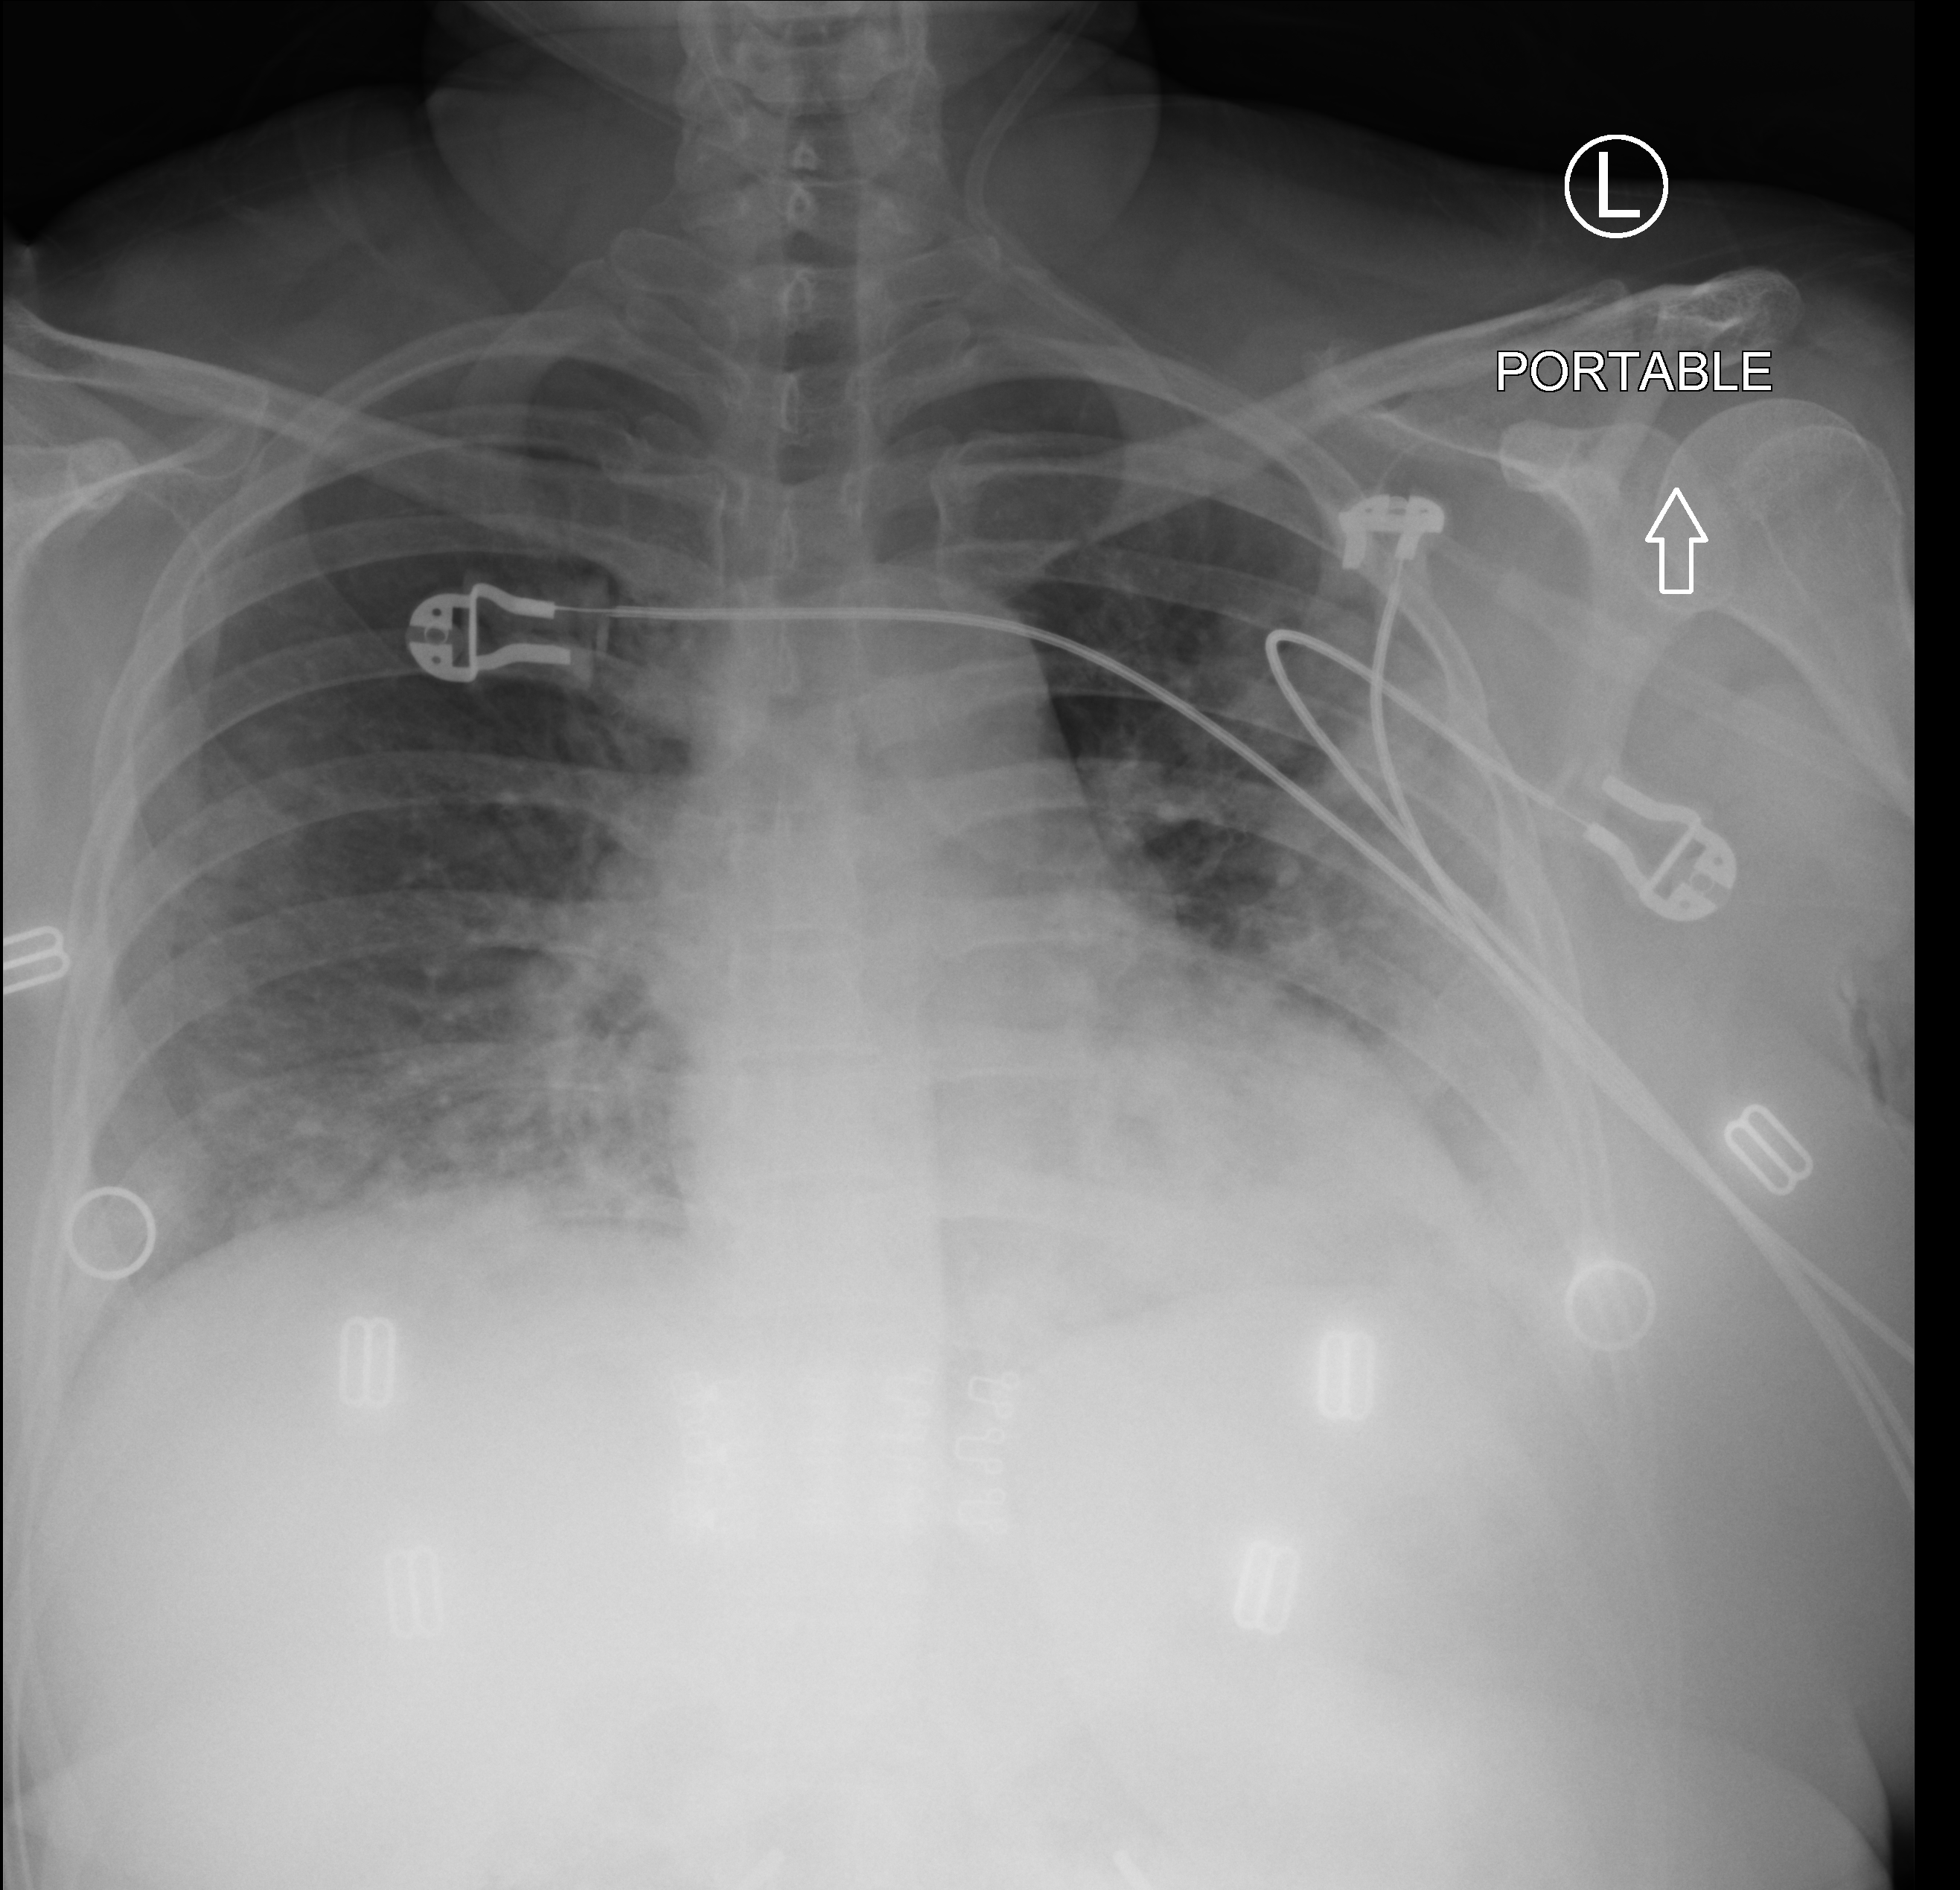
Portable chest radiograph; anteroposterior (AP) projection. Patient hospitalised with COVID-19; female, aged 18–59 years.
Hospital-stay facts (about this admission, not read from this image; timing relative to this image not recorded): smoking status (admission record): never; admitted to intensive care during this hospital stay: no.